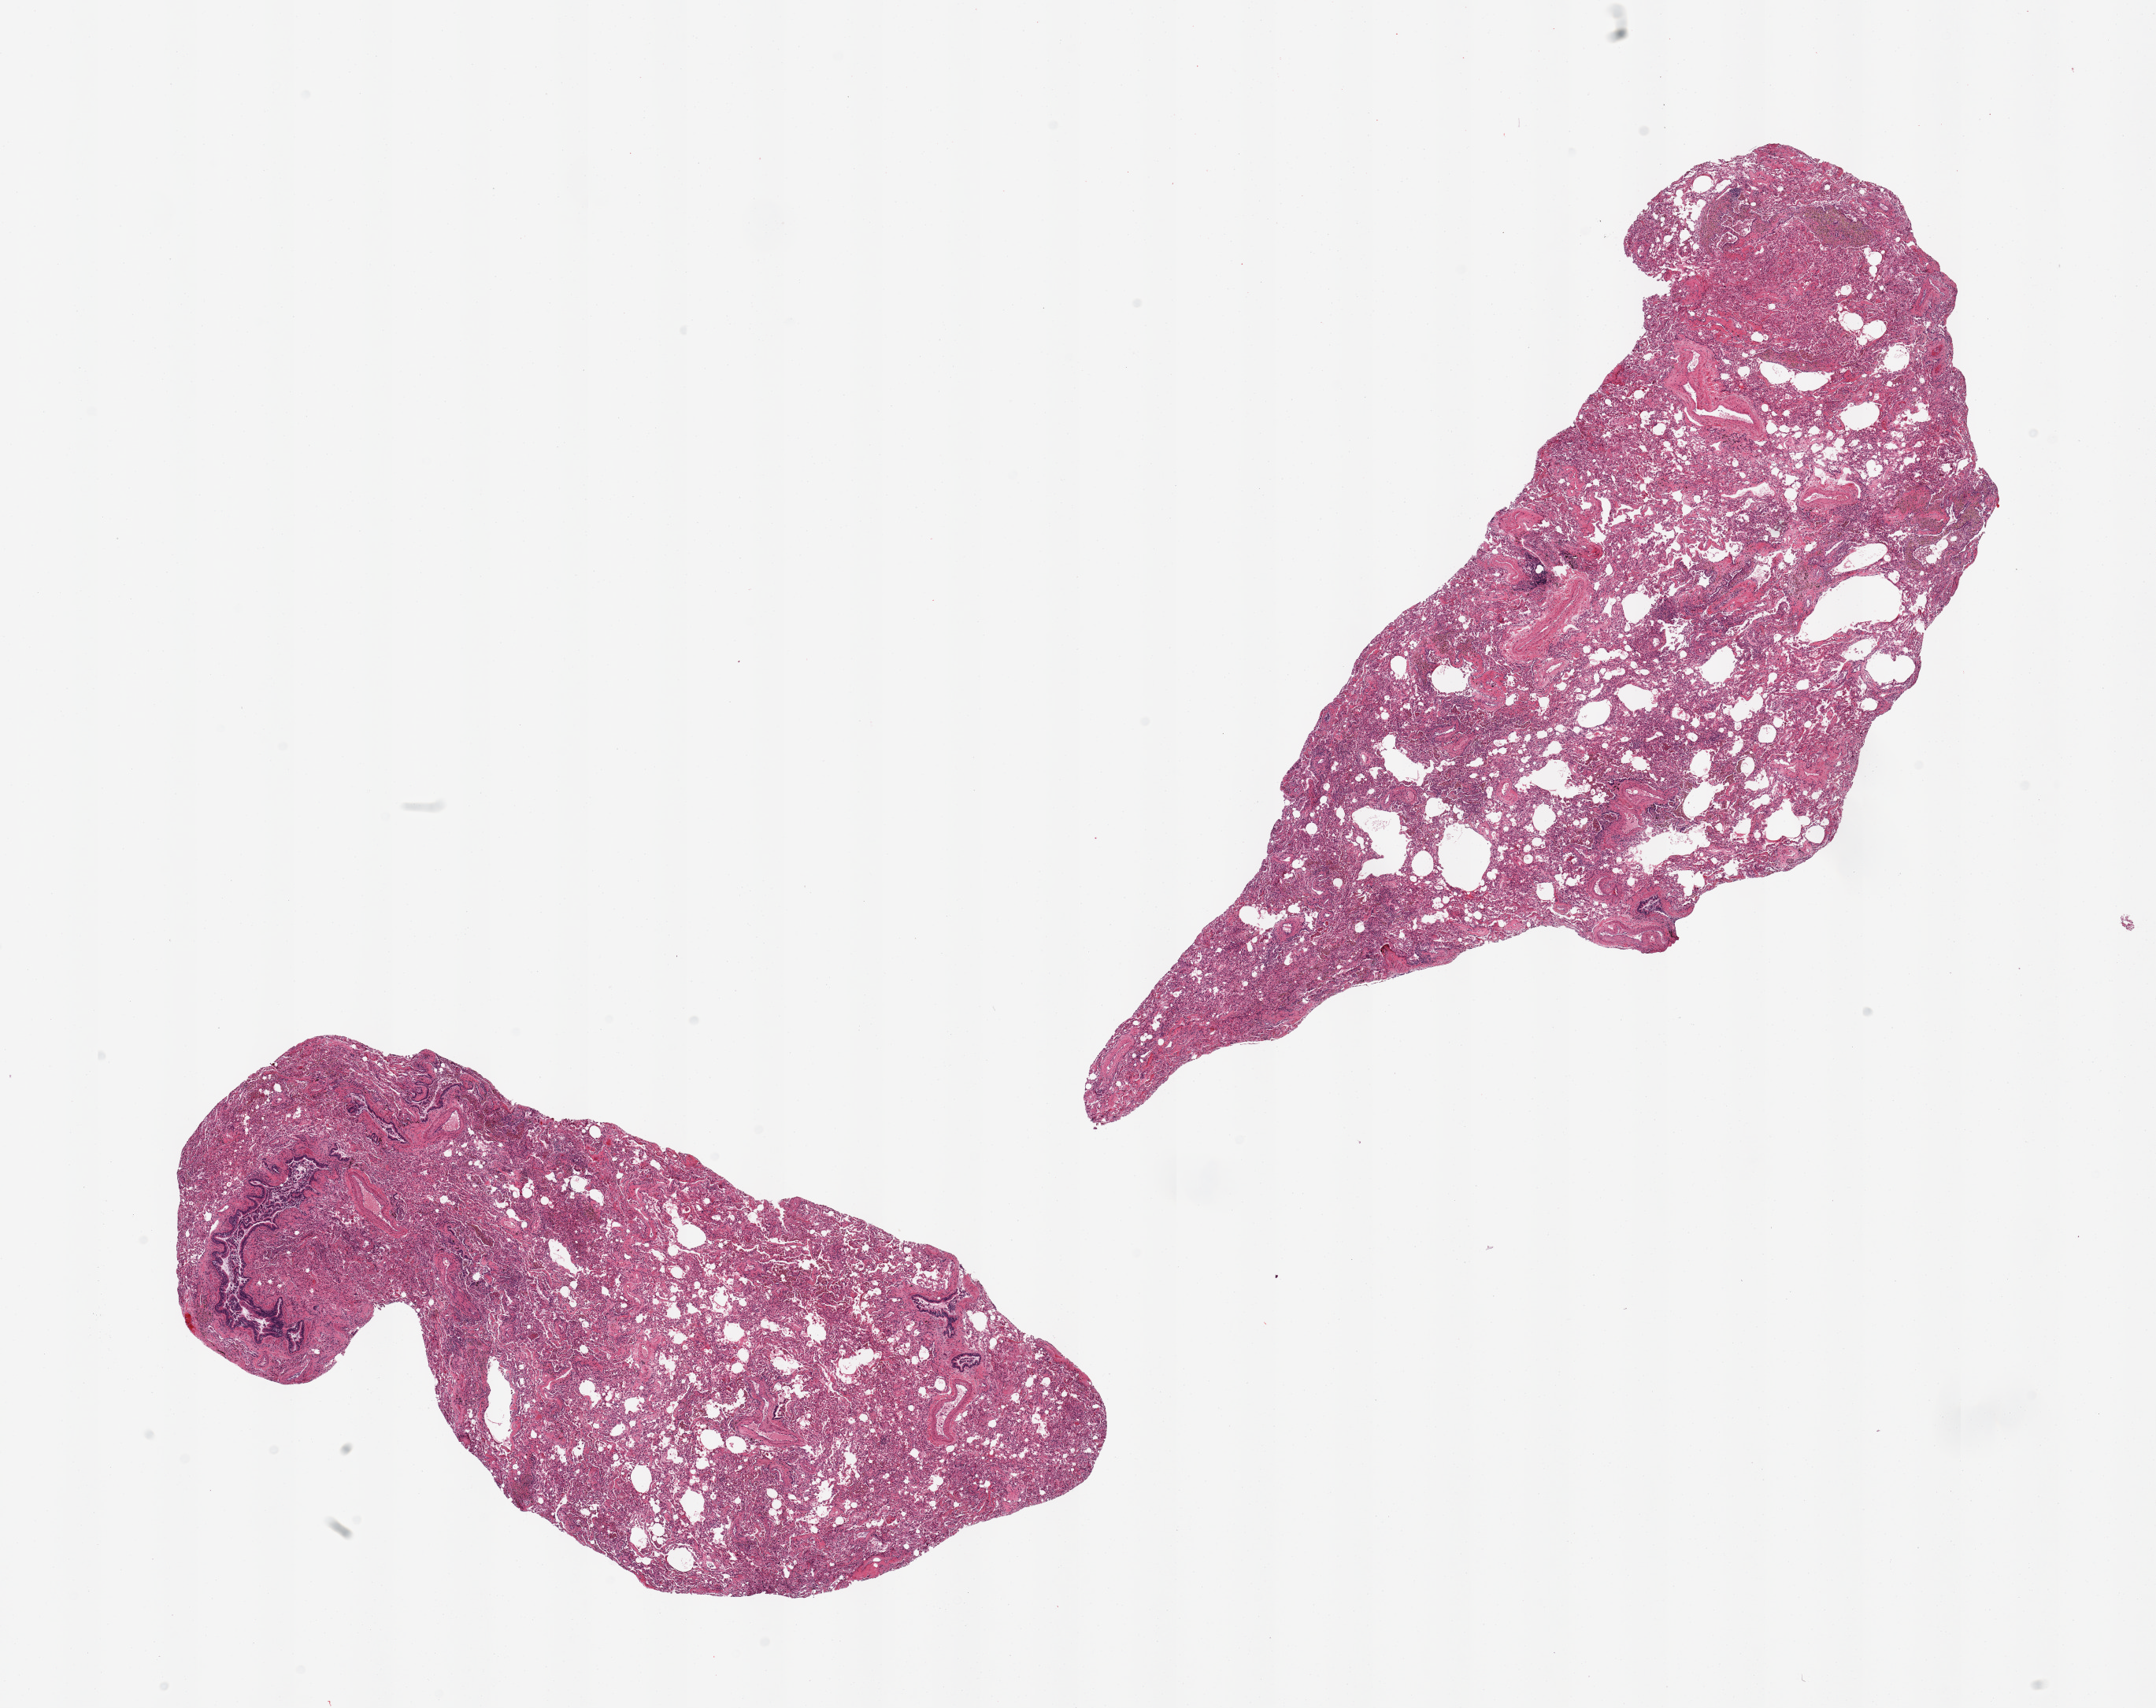
Digitized H&E-stained section, brightfield, low-resolution overview of the scanned area, about 21.7 x 17.2 mm (slide scanned at 20x); PAXgene-fixed, paraffin-embedded tissue; target tissue: lung; tissue donor sample. Donor: female.
Review note (as recorded): 2 pieces; patchy bronchopneumonia; atelectasis; moderate pigmented macrophages.